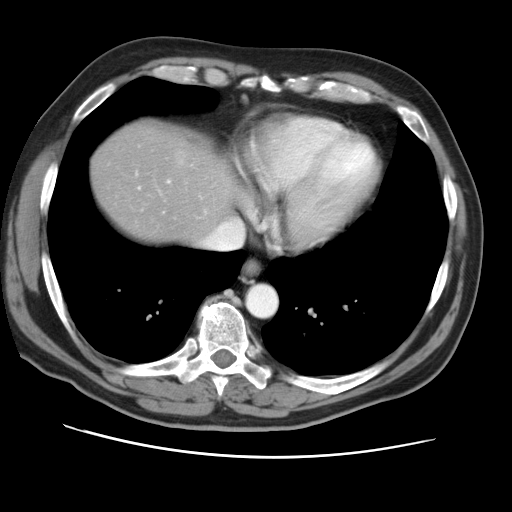
Contrast-enhanced abdominal CT, one axial slice; slice 45 of 49 in the series (ordered by position); 120 kVp; soft-tissue window (W 400 / L 40 HU); 5 mm slice thickness; 512 × 512 image matrix. Male patient, age 59 years. Case-level facts recorded for this patient, not image findings: diagnosis: colorectal cancer liver metastases, imaged before liver resection; multiple liver metastases: yes; largest metastasis: 6.3 cm; chemotherapy before resection: yes.
Outlined on this slice (manually delineated by an expert):
- liver: box from (x=93, y=126) to (x=236, y=240) px
- planned liver remnant (the part of the liver to remain after resection): (x=93, y=126)–(x=236, y=240)
- portal vein (with intrahepatic branches): (x=168, y=180)–(x=170, y=182)
- liver metastasis: (x=175, y=151)–(x=190, y=167)